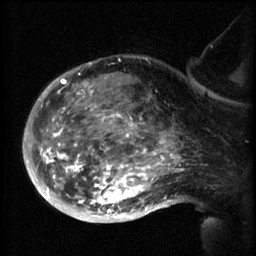
Breast MRI (dynamic contrast-enhanced), one sagittal slice. Slice 42 of 60 in the series (ordered by position). 3 images stored at this slice position (order not interpretable as contrast timing). 1.5 T. TE 4.2 ms, TR 8.2 ms. 256 × 256 image matrix, field of view 200 × 200 mm. Female patient, age 50 years.
Outlined on this slice (semi-automatic segmentation, software-assisted and operator-edited):
- analysis volume of interest (the breast-tissue region the enhancement analysis was run in; not a lesion): box from (x=50, y=64) to (x=169, y=217) px
- tumour enhancement mask (voxels above the 70 % enhancement threshold inside the analysis volume of interest): (x=50, y=74)–(x=169, y=217)